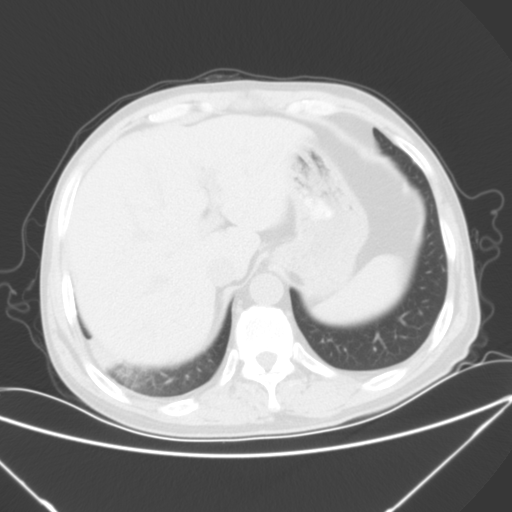
Chest CT, one axial slice. Slice 12 of 57 in the series (ordered by position). Lung window (W 1500 / L -600 HU). 5 mm slice thickness. 512 × 512 image matrix, field of view 364 × 364 mm. Patient: male, 54 years. From the clinical record (not read from this slice): clinical TNM (as recorded): T2 N1 M0; histopathological grade: G3.
Structures marked on this image (bounding box drawn by a radiologist):
- lung tumour (recorded histology: adenocarcinoma): bounding box [x1, y1, x2, y2] px = [86, 333, 119, 370]